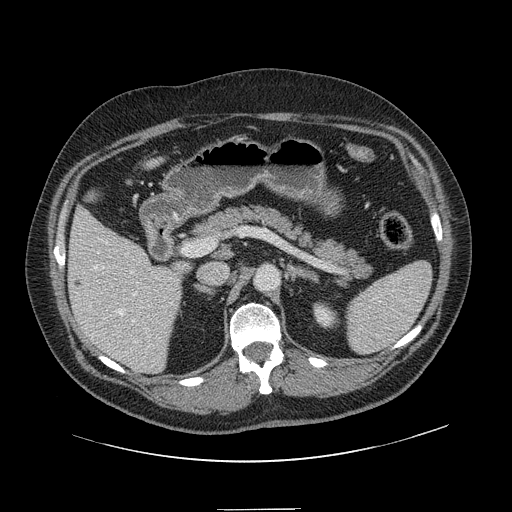
Contrast-enhanced abdominal CT, one axial slice. Position 75 of 154 along the scan axis. 120 kVp. Intravenous contrast given. Soft-tissue window (W 400 / L 40 HU). 512 × 512 image matrix, field of view 451 × 451 mm. Male patient, age 61 years. Case-level facts recorded for this patient, not image findings: diagnosis: colorectal cancer liver metastases, imaged before liver resection; multiple liver metastases: yes; largest metastasis: 2.6 cm; disease in both lobes: yes.
Annotated regions visible in this slice (outlined manually by an expert reader):
- hepatic veins: bounding box (x1, y1, x2, y2) in pixels: (94, 265, 137, 351)
- liver: (69, 210, 182, 372)
- planned liver remnant (the part of the liver to remain after resection): (69, 209, 182, 365)
- portal vein (with intrahepatic branches): (130, 270, 141, 322)
- liver metastasis: (73, 280, 83, 292)